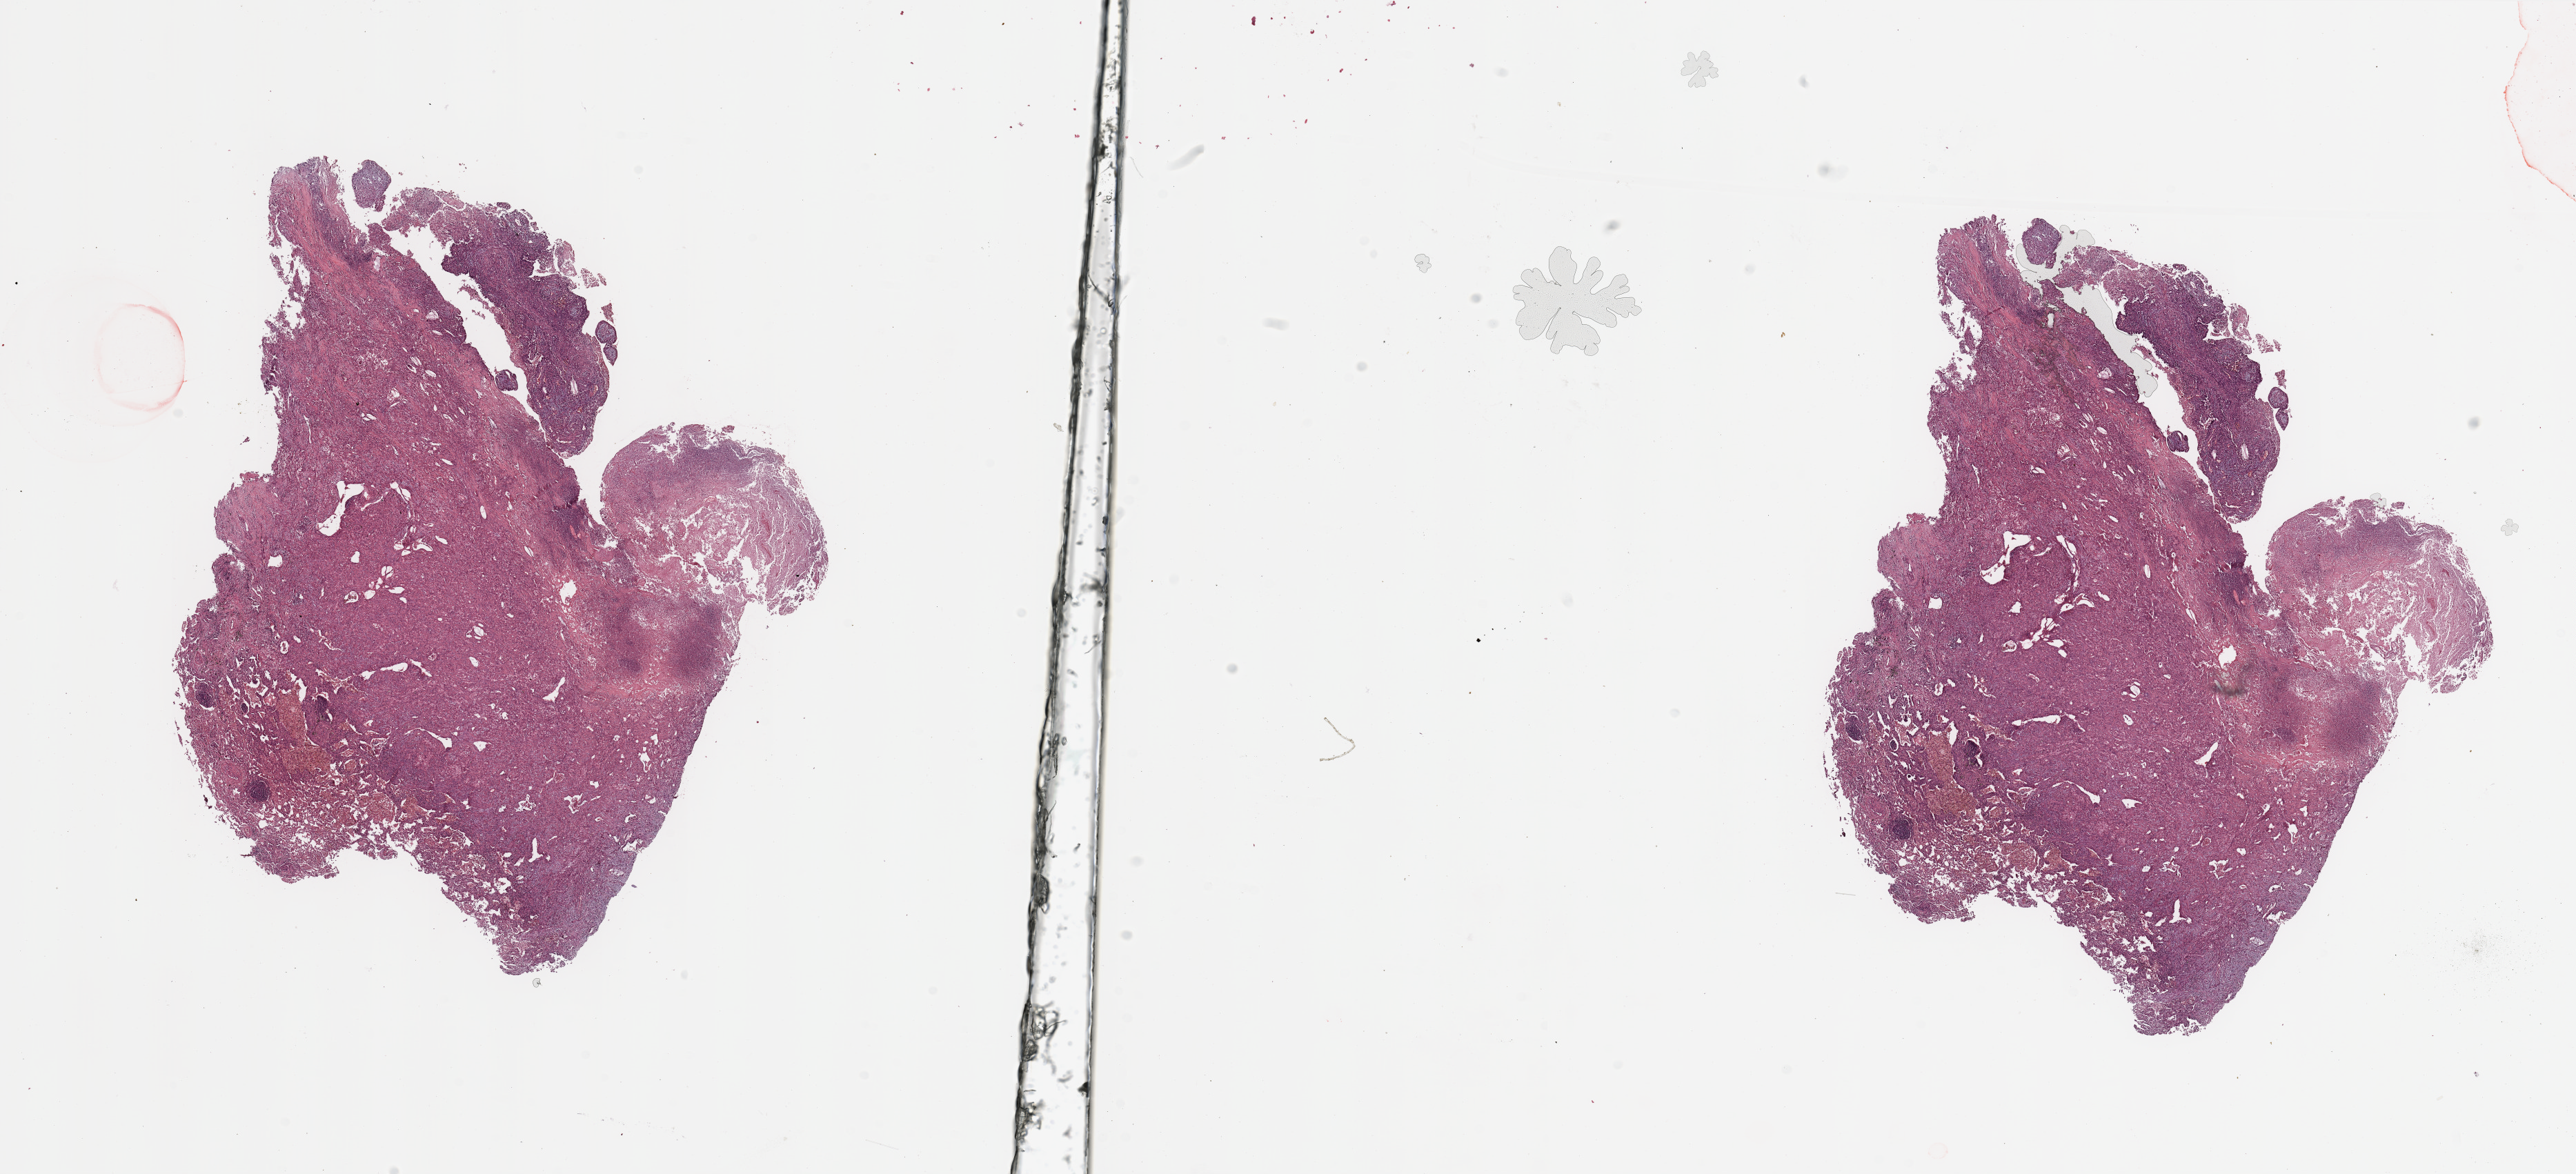
Digitized H&E tissue section (whole slide), low-resolution overview of the scanned area, about 29.5 x 13.5 mm; lung, tumour tissue. Patient: male, age 78 years. Histologic grade: G2 (moderately differentiated).
AJCC pathologic stage: IIA. Histologic diagnosis: Squamous cell carcinoma, NOS. Primary tumour site (as recorded): left upper lobe.